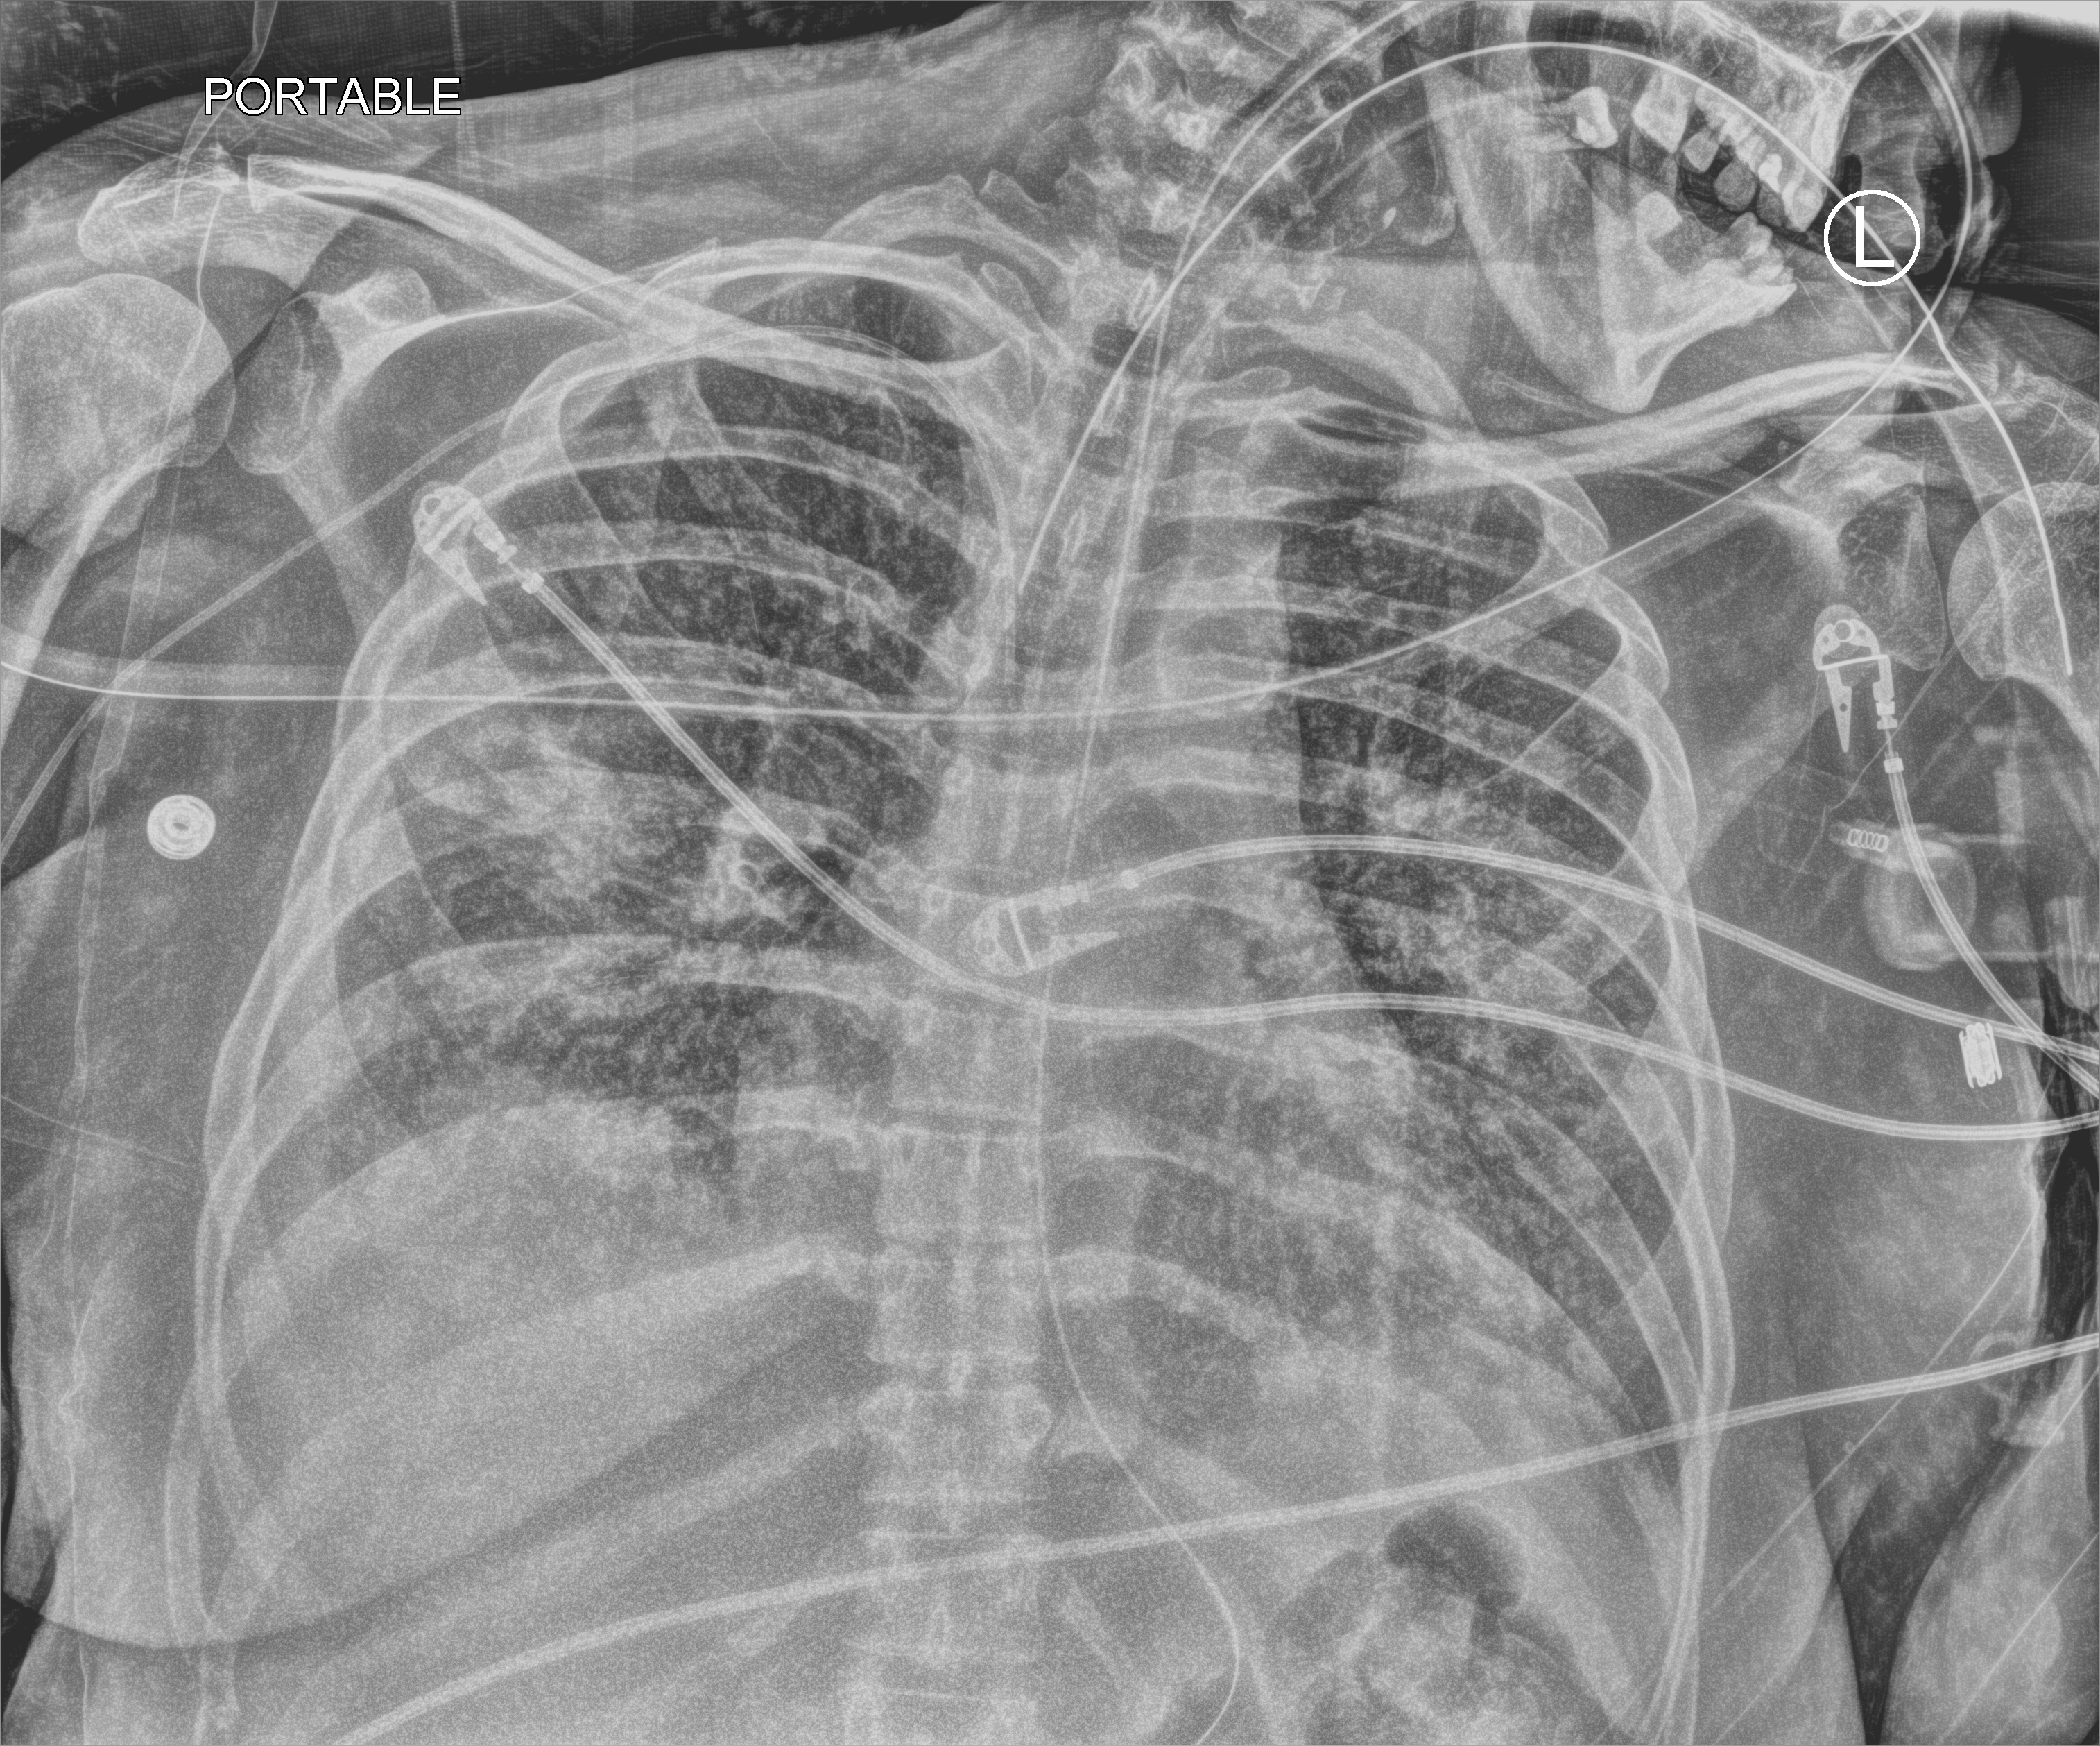
Portable chest radiograph. Patient hospitalised with COVID-19, aged 18–59 years.
Admission-level facts for this patient (not findings on this image; timing relative to this image not recorded):
- admitted to intensive care during this hospital stay: yes
- hypertension (admission record): no